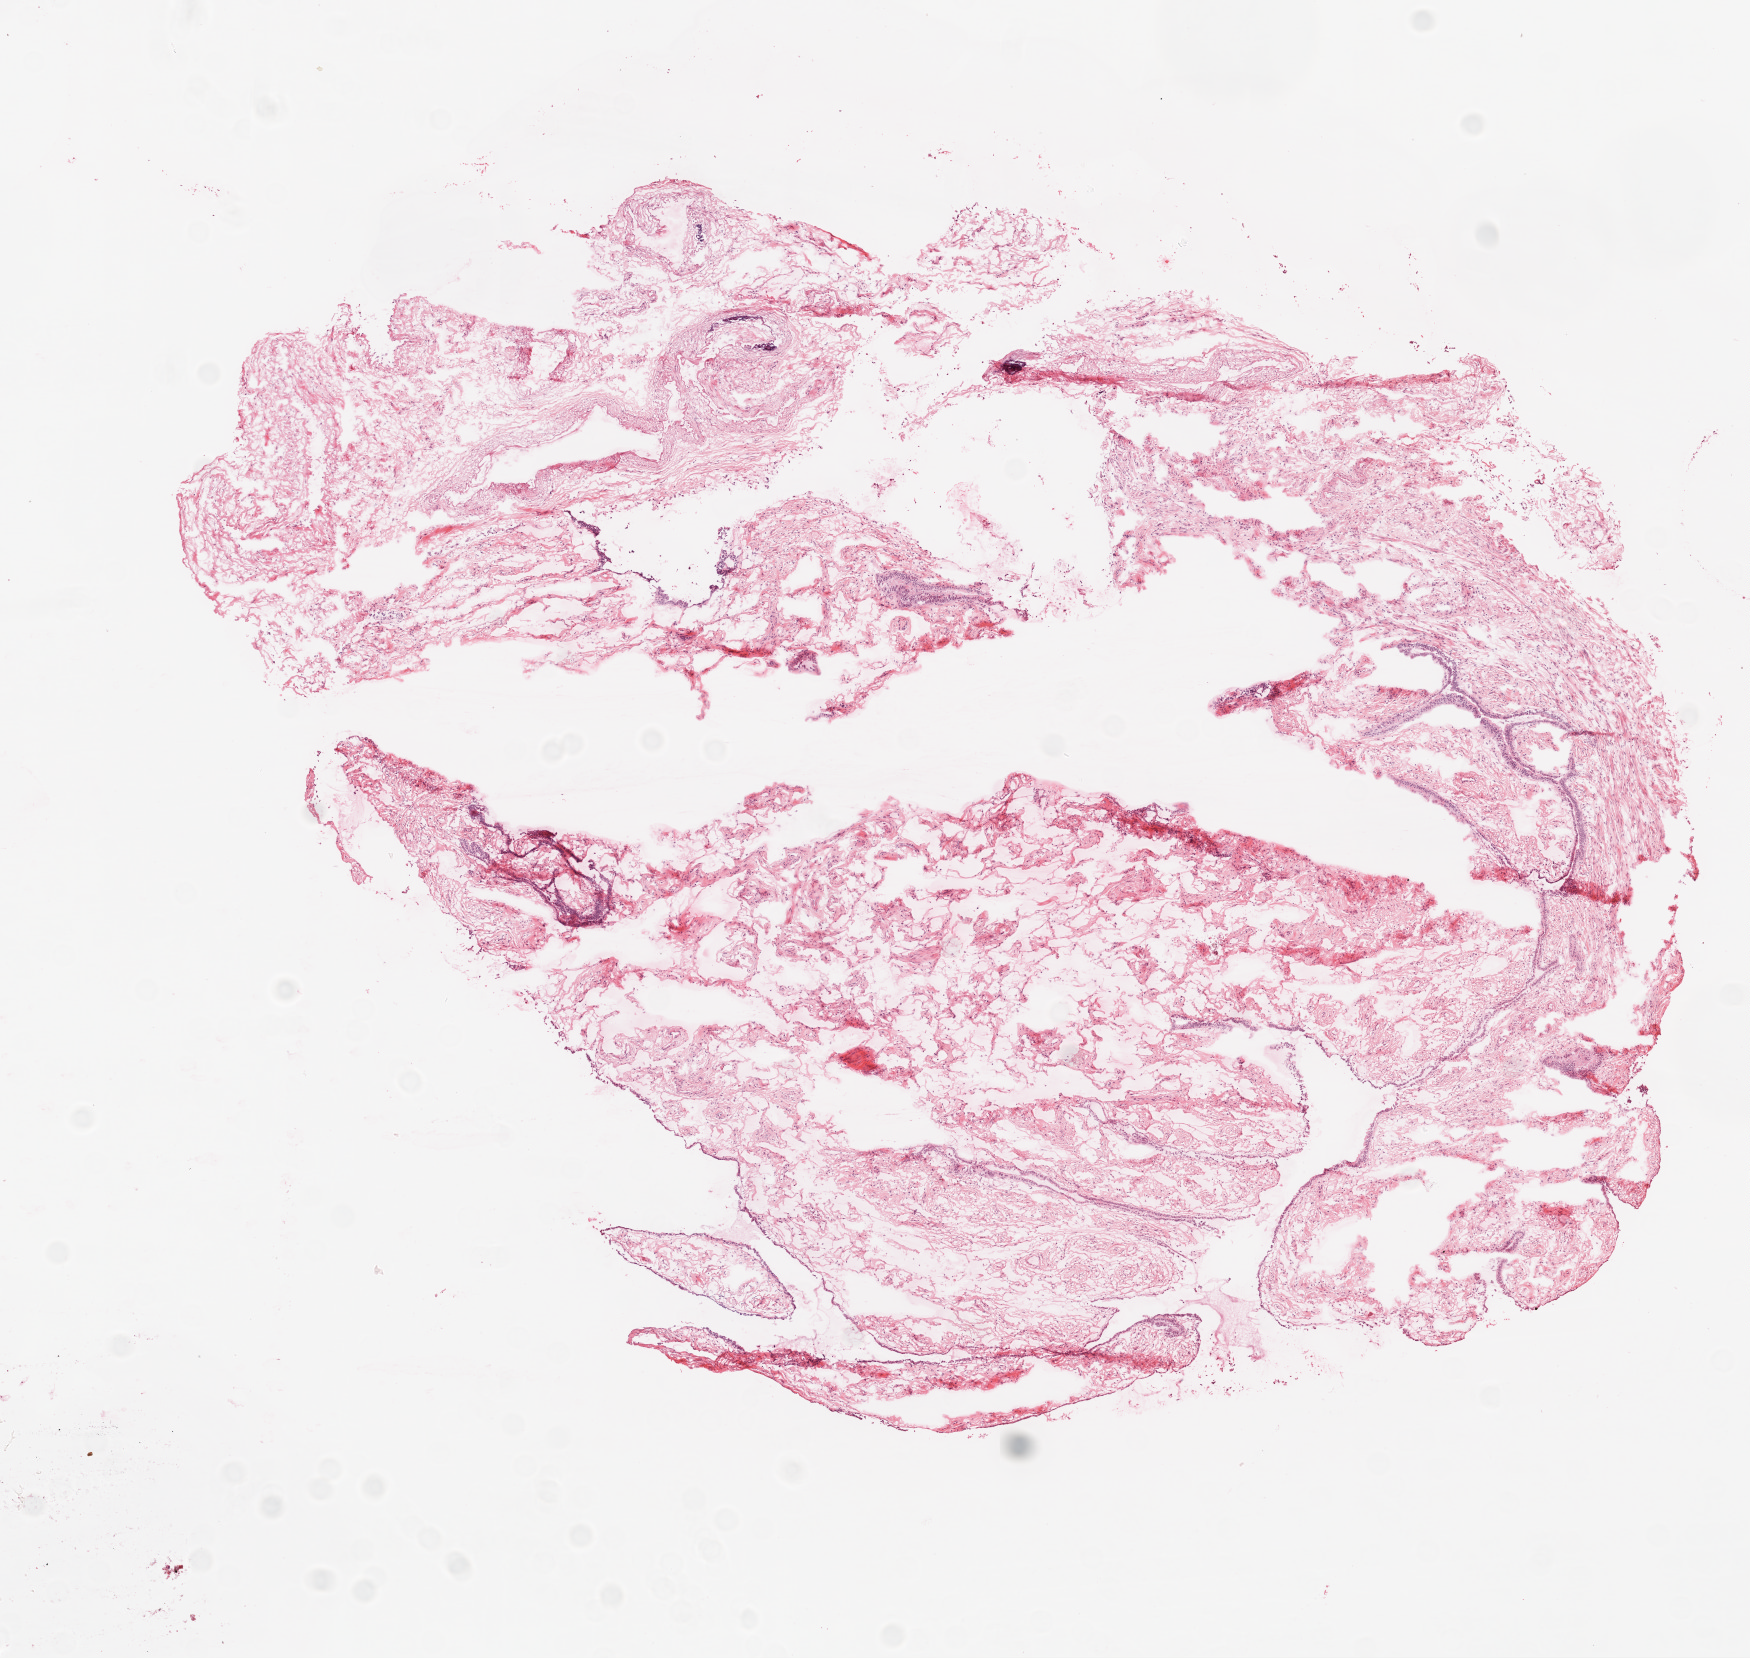
Whole-slide histology image, H&E-stained, low-resolution overview of the scanned area, about 7.0 x 6.7 mm (slide scanned at 20x). Frozen section from the top of the tissue portion. Ovary, solid tissue normal (non-tumour tissue) sample. Female patient; age at initial diagnosis 73 years.
This section: solid tissue normal sample (biorepository sample class). Patient diagnosis: Serous cystadenocarcinoma, NOS.